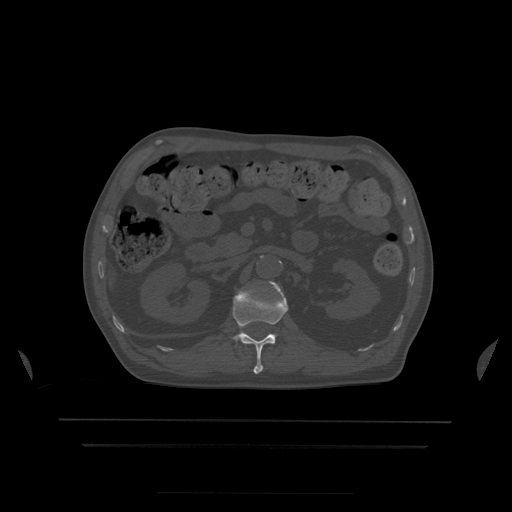
CT including the spine, one axial slice; position 167 of 522 along the scan axis; bone window (W 1800 / L 400 HU); 1.25 mm slice thickness; 512 × 512 image matrix, field of view 436 × 436 mm. Patient age 68 years. From the clinical record (not read from this slice): primary cancer: urothelial.
Annotated regions visible in this slice (semi-automatically segmented with operator editing):
- L1 vertebra: bounding box [x1, y1, x2, y2] px = [233, 282, 288, 375]
- L2 vertebra: [270, 282, 279, 287]